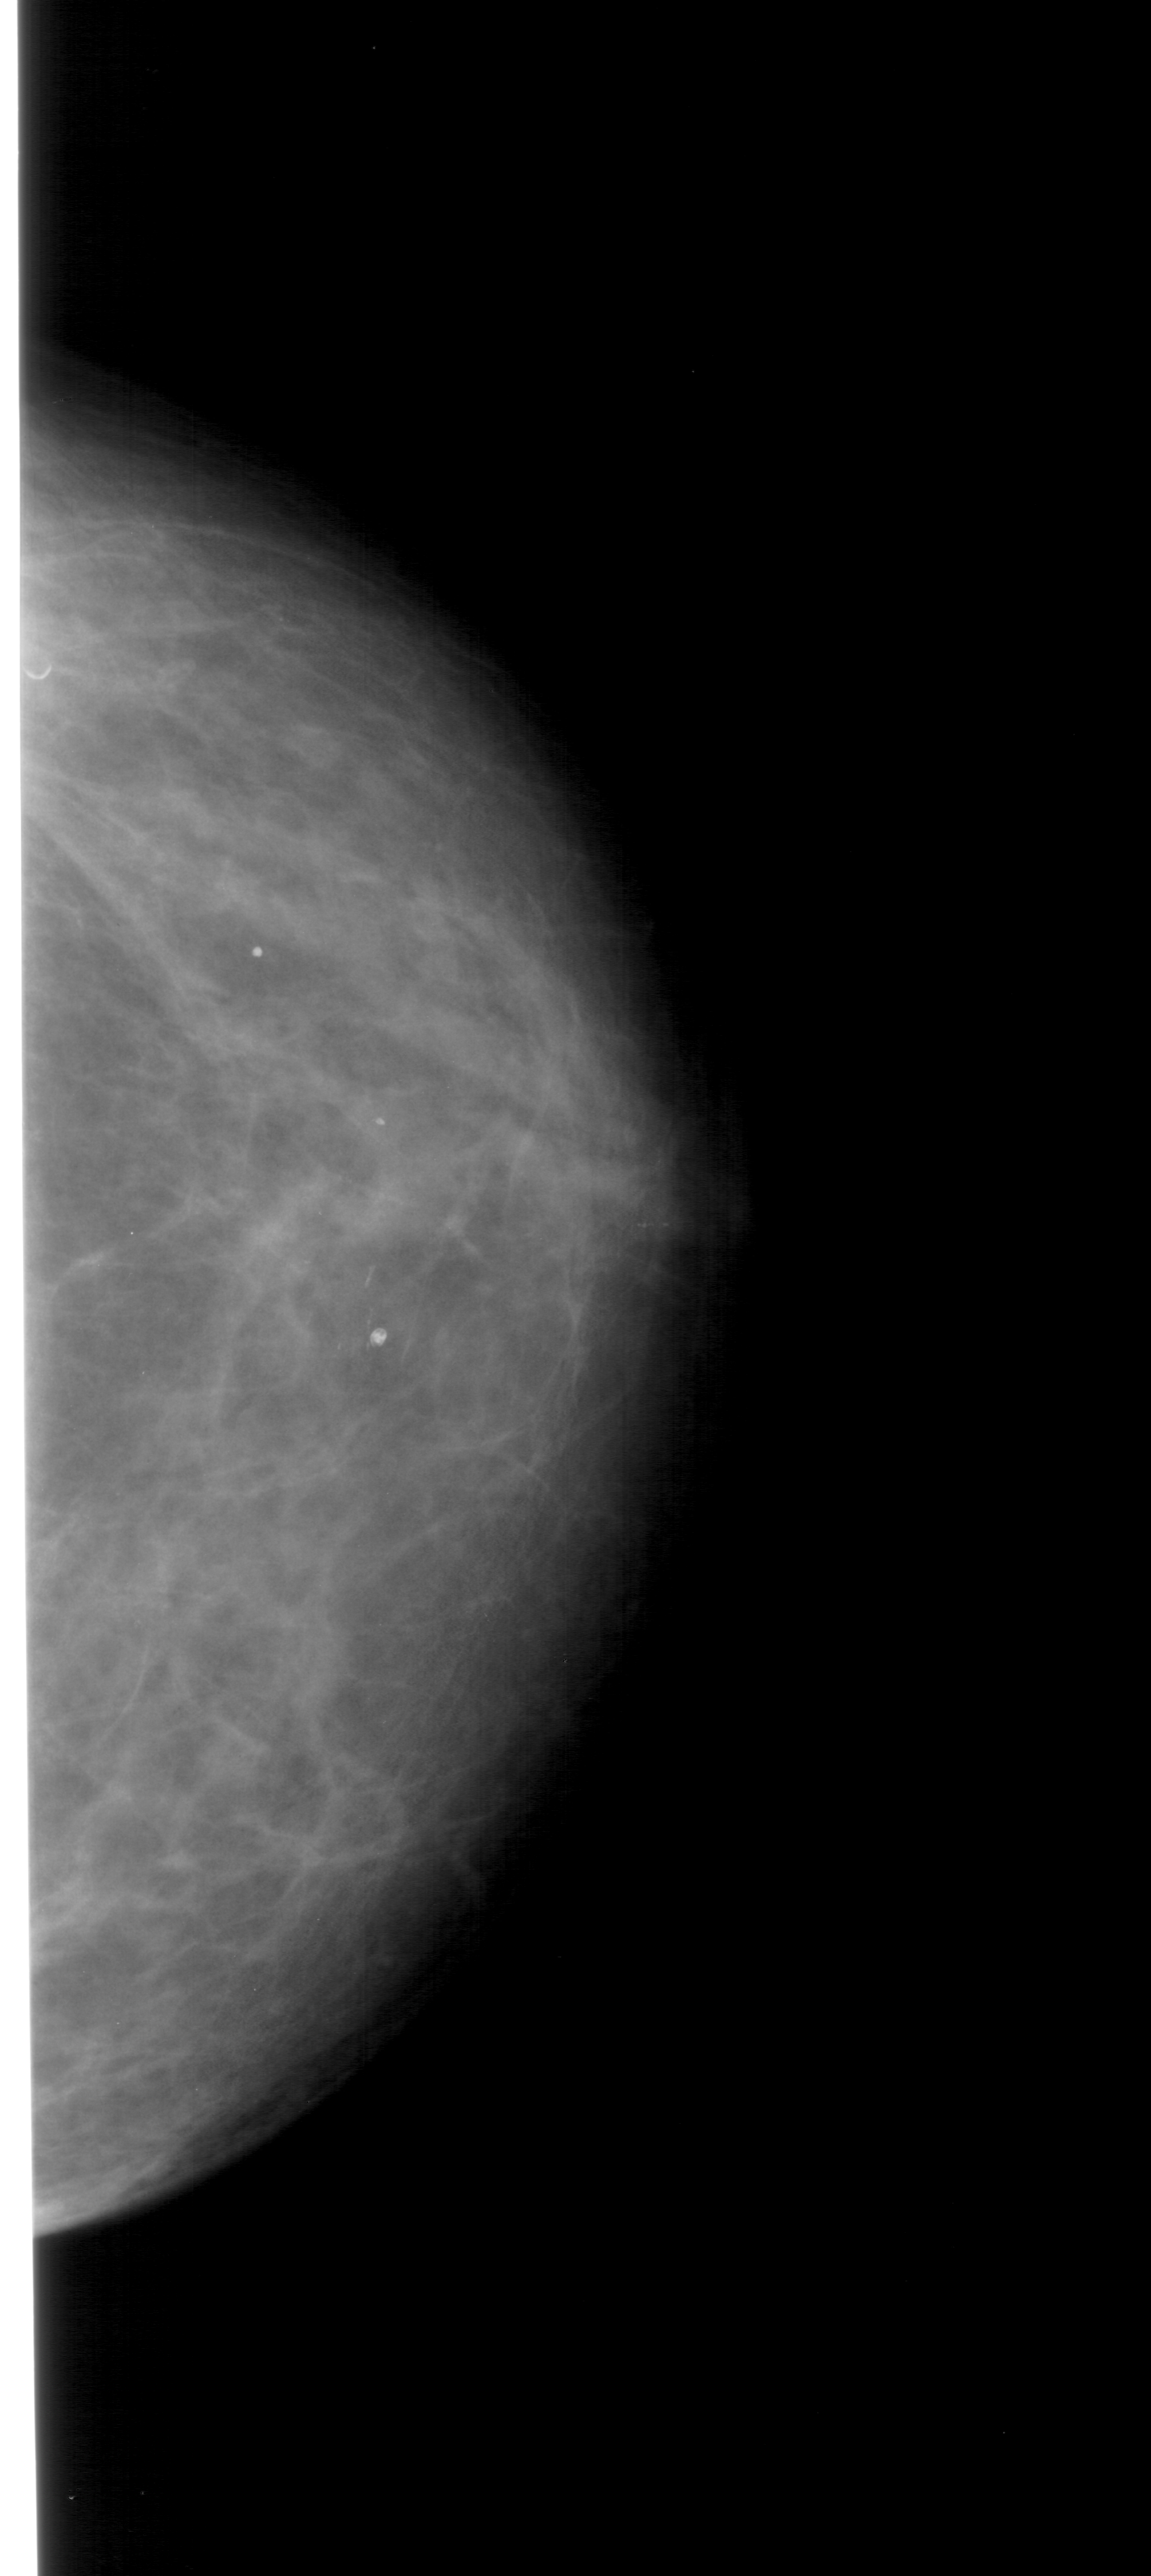
Digitized screen-film mammogram, right breast, craniocaudal (CC) view, breast composition: scattered fibroglandular densities (BI-RADS density category 2 of 4).
Finding: calcifications, morphology pleomorphic, distribution clustered; BI-RADS assessment category 4; pathology result (as recorded, not read from the image): malignant.